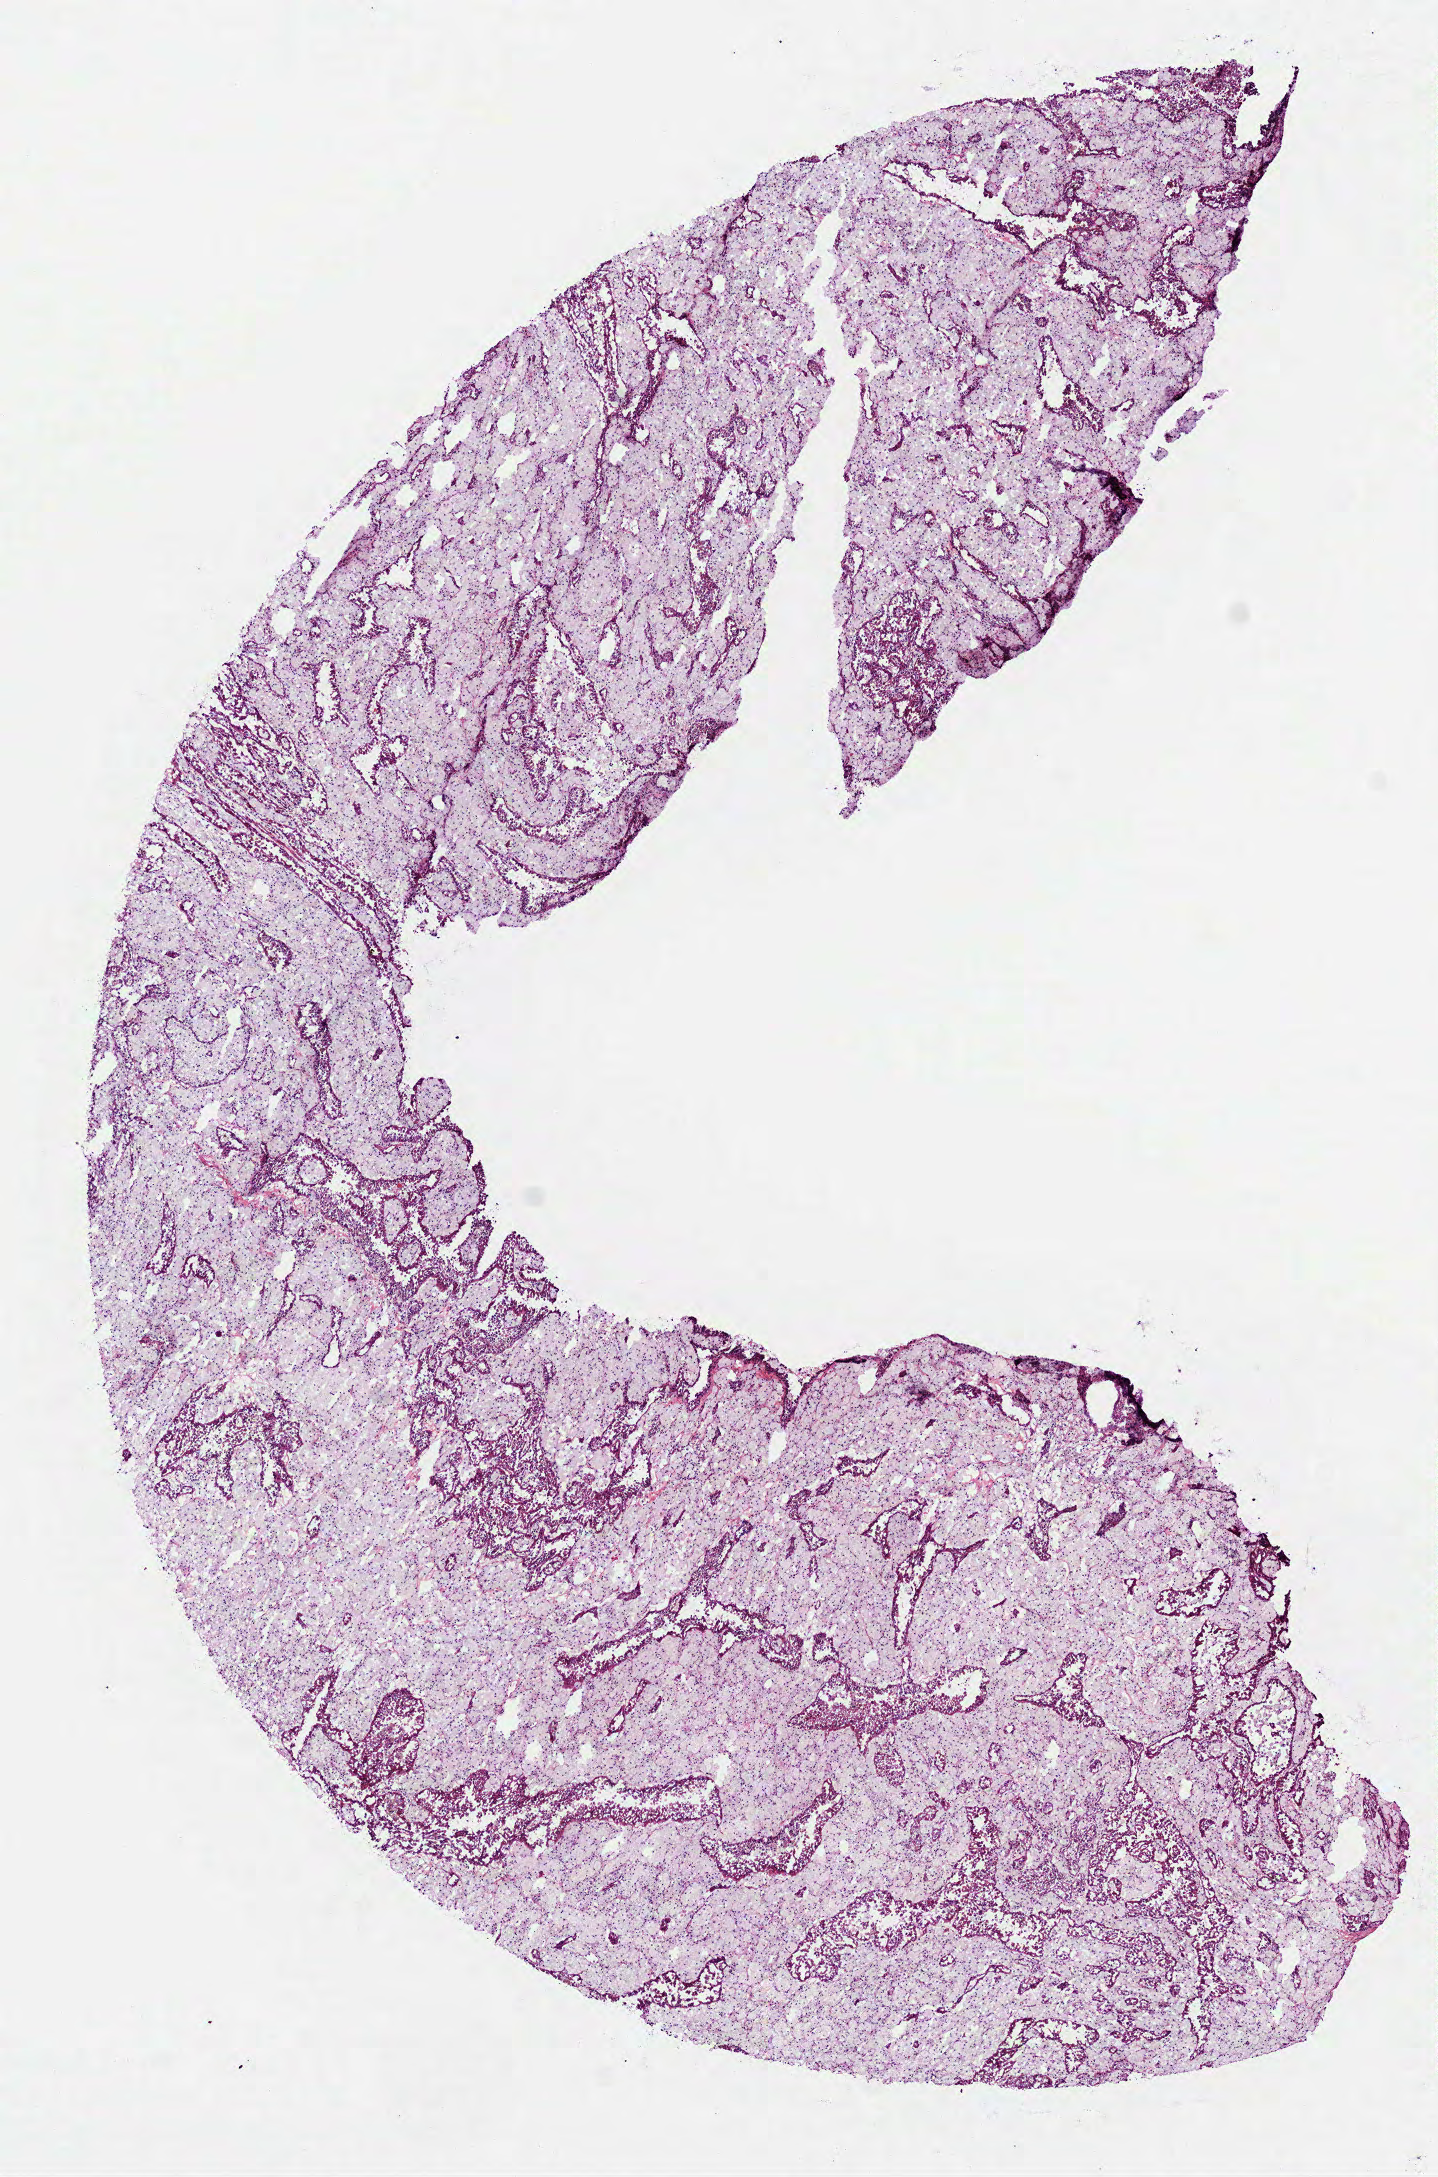
Whole-slide histology image, H&E, shown as a low-resolution overview of the whole scanned area (about 5.8 x 8.8 mm, acquisition: 40x scan). Frozen section from the top of the tissue portion. Sample: primary tumour, kidney. Patient sex: male. Slide review estimates, as recorded: tumour cells 100%, tumour nuclei 65%, normal cells 0%, stromal cells 0%, necrosis 0%. Inflammatory infiltration, as recorded: lymphocyte infiltration 2%, monocyte infiltration 30%, neutrophil infiltration 0%.
AJCC pathologic stage: I (6th edition). Diagnosis: Papillary adenocarcinoma, NOS.